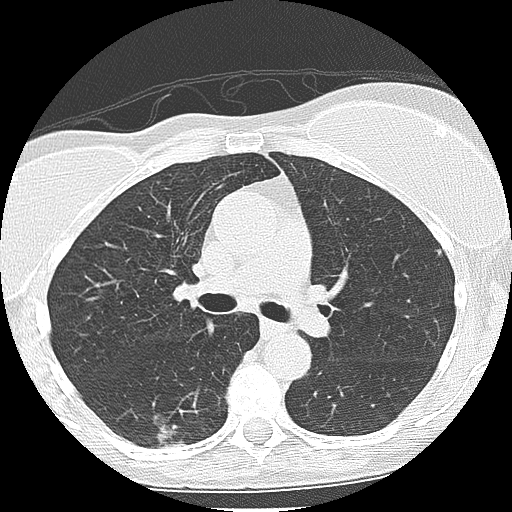
Low-dose screening chest CT, one axial slice. Slice 131 of 225 in the series (ordered by position). Reconstruction kernel LUNG. 120 kVp. Lung window (W 1500 / L -600 HU). 512 × 512 image matrix, field of view 300 × 300 mm.
Structures marked on this image (manually delineated by an expert):
- lesion 1 (tumor, lower lobe of right lung): bounding box [x1, y1, x2, y2] px = [158, 425, 186, 449]